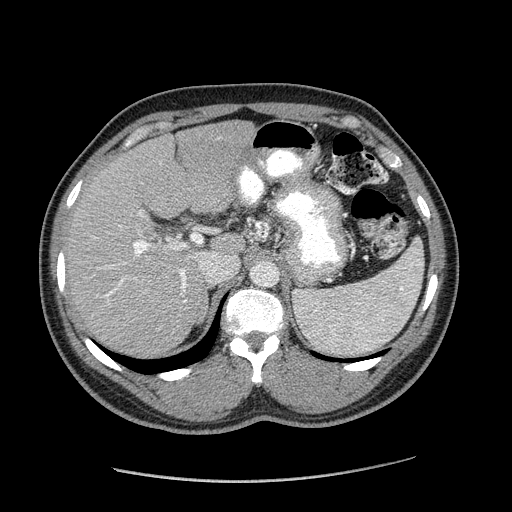
Contrast-enhanced abdominal CT (liver protocol), one axial slice; slice 121 of 182 in the series (ordered by position); reconstruction kernel STANDARD; 120 kVp; soft-tissue window (W 400 / L 40 HU); 512 × 512 image matrix, field of view 400 × 400 mm. From the clinical record (not read from this slice): diagnosis: hepatocellular carcinoma (patient treated with transarterial chemoembolisation; whether this scan precedes or follows treatment is not stated here); TNM stage (as recorded): Stage-I; Child-Pugh class: A; tumour differentiation: well differentiated; tumour nodularity: uninodular.
Outlined on this slice (semi-automatic segmentation, software-assisted and operator-edited):
- liver parenchyma outside the tumour (the mass and vessels are separate outlines, so this box may not span the whole liver): bounding box [x1, y1, x2, y2] px = [66, 120, 254, 356]
- liver vessels: [95, 212, 232, 302]